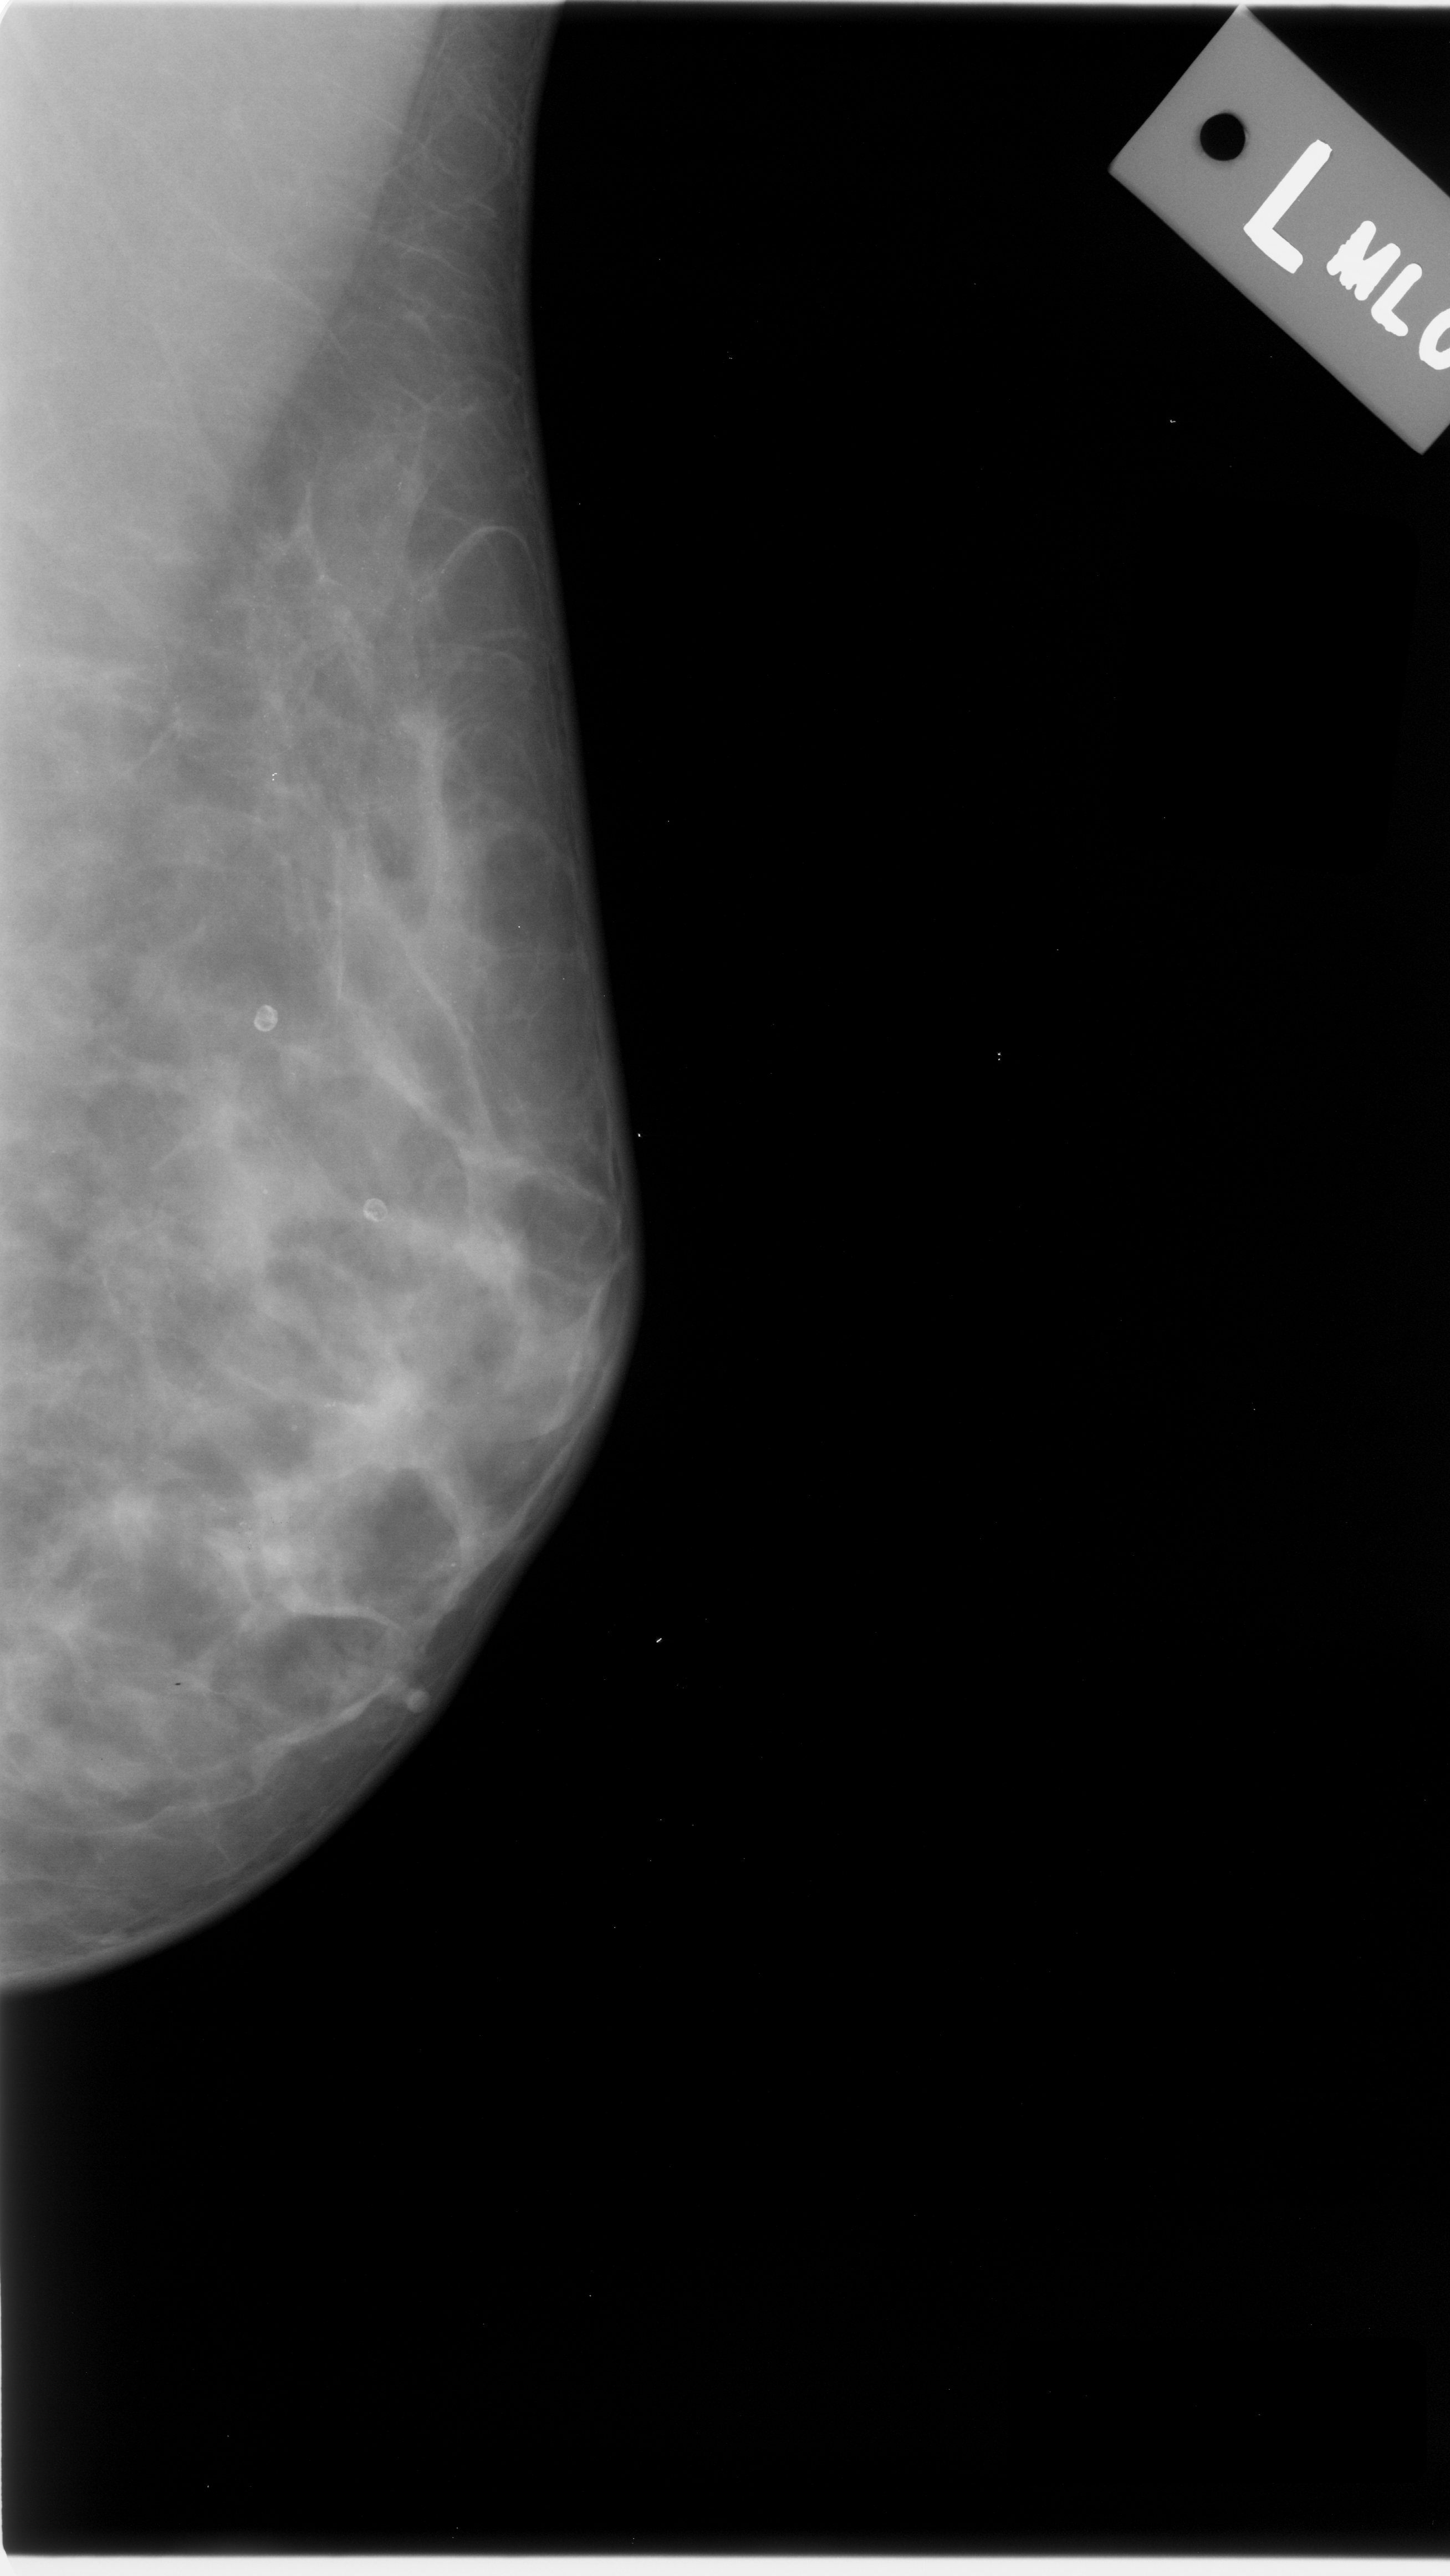
Digitized screen-film mammogram. Left breast. MLO view. BI-RADS breast density category 2 (scale 1–4). 1450 × 2576 image matrix.
Expert-marked regions of interest on this film, with their recorded descriptors:
- calcifications, morphology amorphous, distribution diffusely scattered; BI-RADS assessment category 3; subtlety rating 4 on a 1 (subtle) to 5 (obvious) scale; pathology (as recorded): malignant: box from (x=0, y=399) to (x=586, y=1739) px